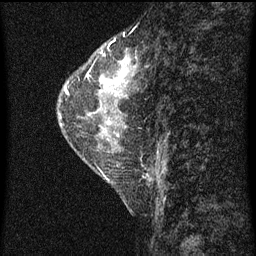
Breast MRI (dynamic contrast-enhanced), one sagittal slice; position 25 of 60 along the scan axis; dynamic contrast-enhanced series, image 2 of 4 at this slice position (ordered by acquisition); 1.5 T; TE 4.2 ms, TR 8 ms; 2 mm slice thickness; 256 × 256 image matrix, field of view 180 × 180 mm. Patient: female, 56 years.
Outlined on this slice (semi-automatically segmented with operator editing):
- analysis volume of interest (the breast-tissue region the enhancement analysis was run in; not a lesion): bounding box [x1, y1, x2, y2] px = [59, 52, 134, 115]
- tumour enhancement mask (voxels above the 70 % enhancement threshold inside the analysis volume of interest): [66, 68, 126, 91]